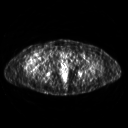
FDG PET of an extremity soft-tissue mass (from a PET/CT study), one axial slice. Position 284 of 311 along the scan axis. 3.27 mm slice thickness. 128 × 128 image matrix, field of view 500 × 500 mm. Female patient, age 57 years. From the clinical record (not read from this slice): histological type: pleiomorphic undifferentiated sarcoma; grade: high; site of the primary tumour: right quadricep.
Outlined on this slice (expert contour drawn on MRI and transferred to this co-registered scan by the dataset authors):
- tumour plus oedema (research contour): bounding box (x1, y1, x2, y2) in pixels: (25, 52, 41, 68)